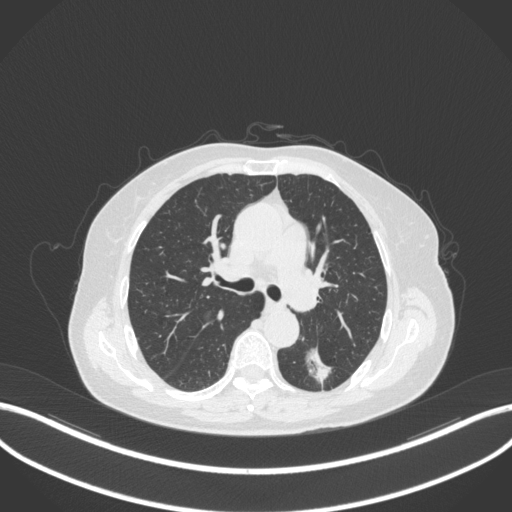
Chest CT, one axial slice; position 188 of 352 along the scan axis; lung window (W 1500 / L -600 HU); 1 mm slice thickness; 512 × 512 image matrix, field of view 400 × 400 mm. Patient: female, 70 years. Case-level facts recorded for this patient, not image findings: clinical TNM (as recorded): T1c N0 M0.
Annotated regions visible in this slice (rectangle marked by the reading radiologist):
- lung tumour (recorded histology: adenocarcinoma): bounding box <296,341,338,389> (left, top, right, bottom; pixels)